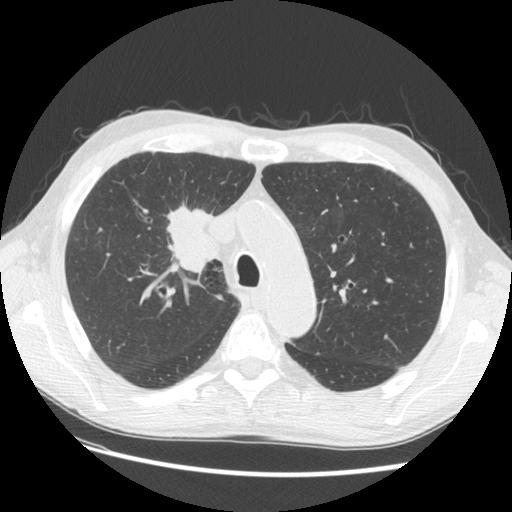
Low-dose screening chest CT, one axial slice. Slice 97 of 133 in the series (ordered by position). Reconstruction kernel STANDARD. 120 kVp. Lung window (W 1500 / L -600 HU). 2.5 mm slice thickness. 512 × 512 image matrix, field of view 360 × 360 mm.
Structures marked on this image (outlined manually by an expert reader):
- lesion 1 (tumor, hilum of right lung): box from (x=166, y=205) to (x=218, y=273) px